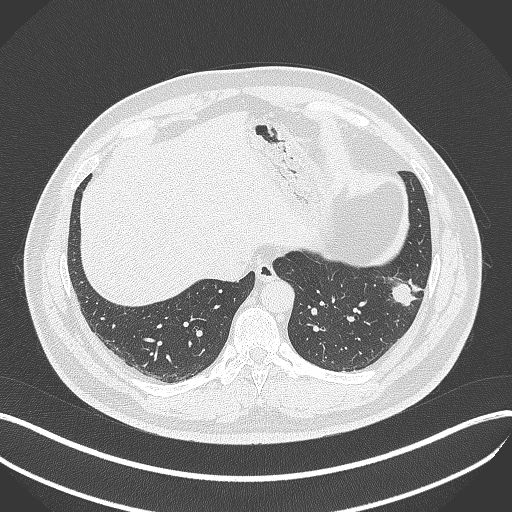
Chest CT, one axial slice. Slice 113 of 429 in the series (ordered by position). Reconstruction kernel B70f. 120 kVp. Lung window (W 1500 / L -600 HU). 512 × 512 image matrix, field of view 400 × 400 mm. Patient: male, 39 years. Case-level facts recorded for this patient, not image findings: clinical TNM (as recorded): T2a N0 M0.
Annotated regions visible in this slice (rectangle marked by the reading radiologist):
- lung tumour (recorded histology: adenocarcinoma): box from (x=383, y=269) to (x=424, y=308) px